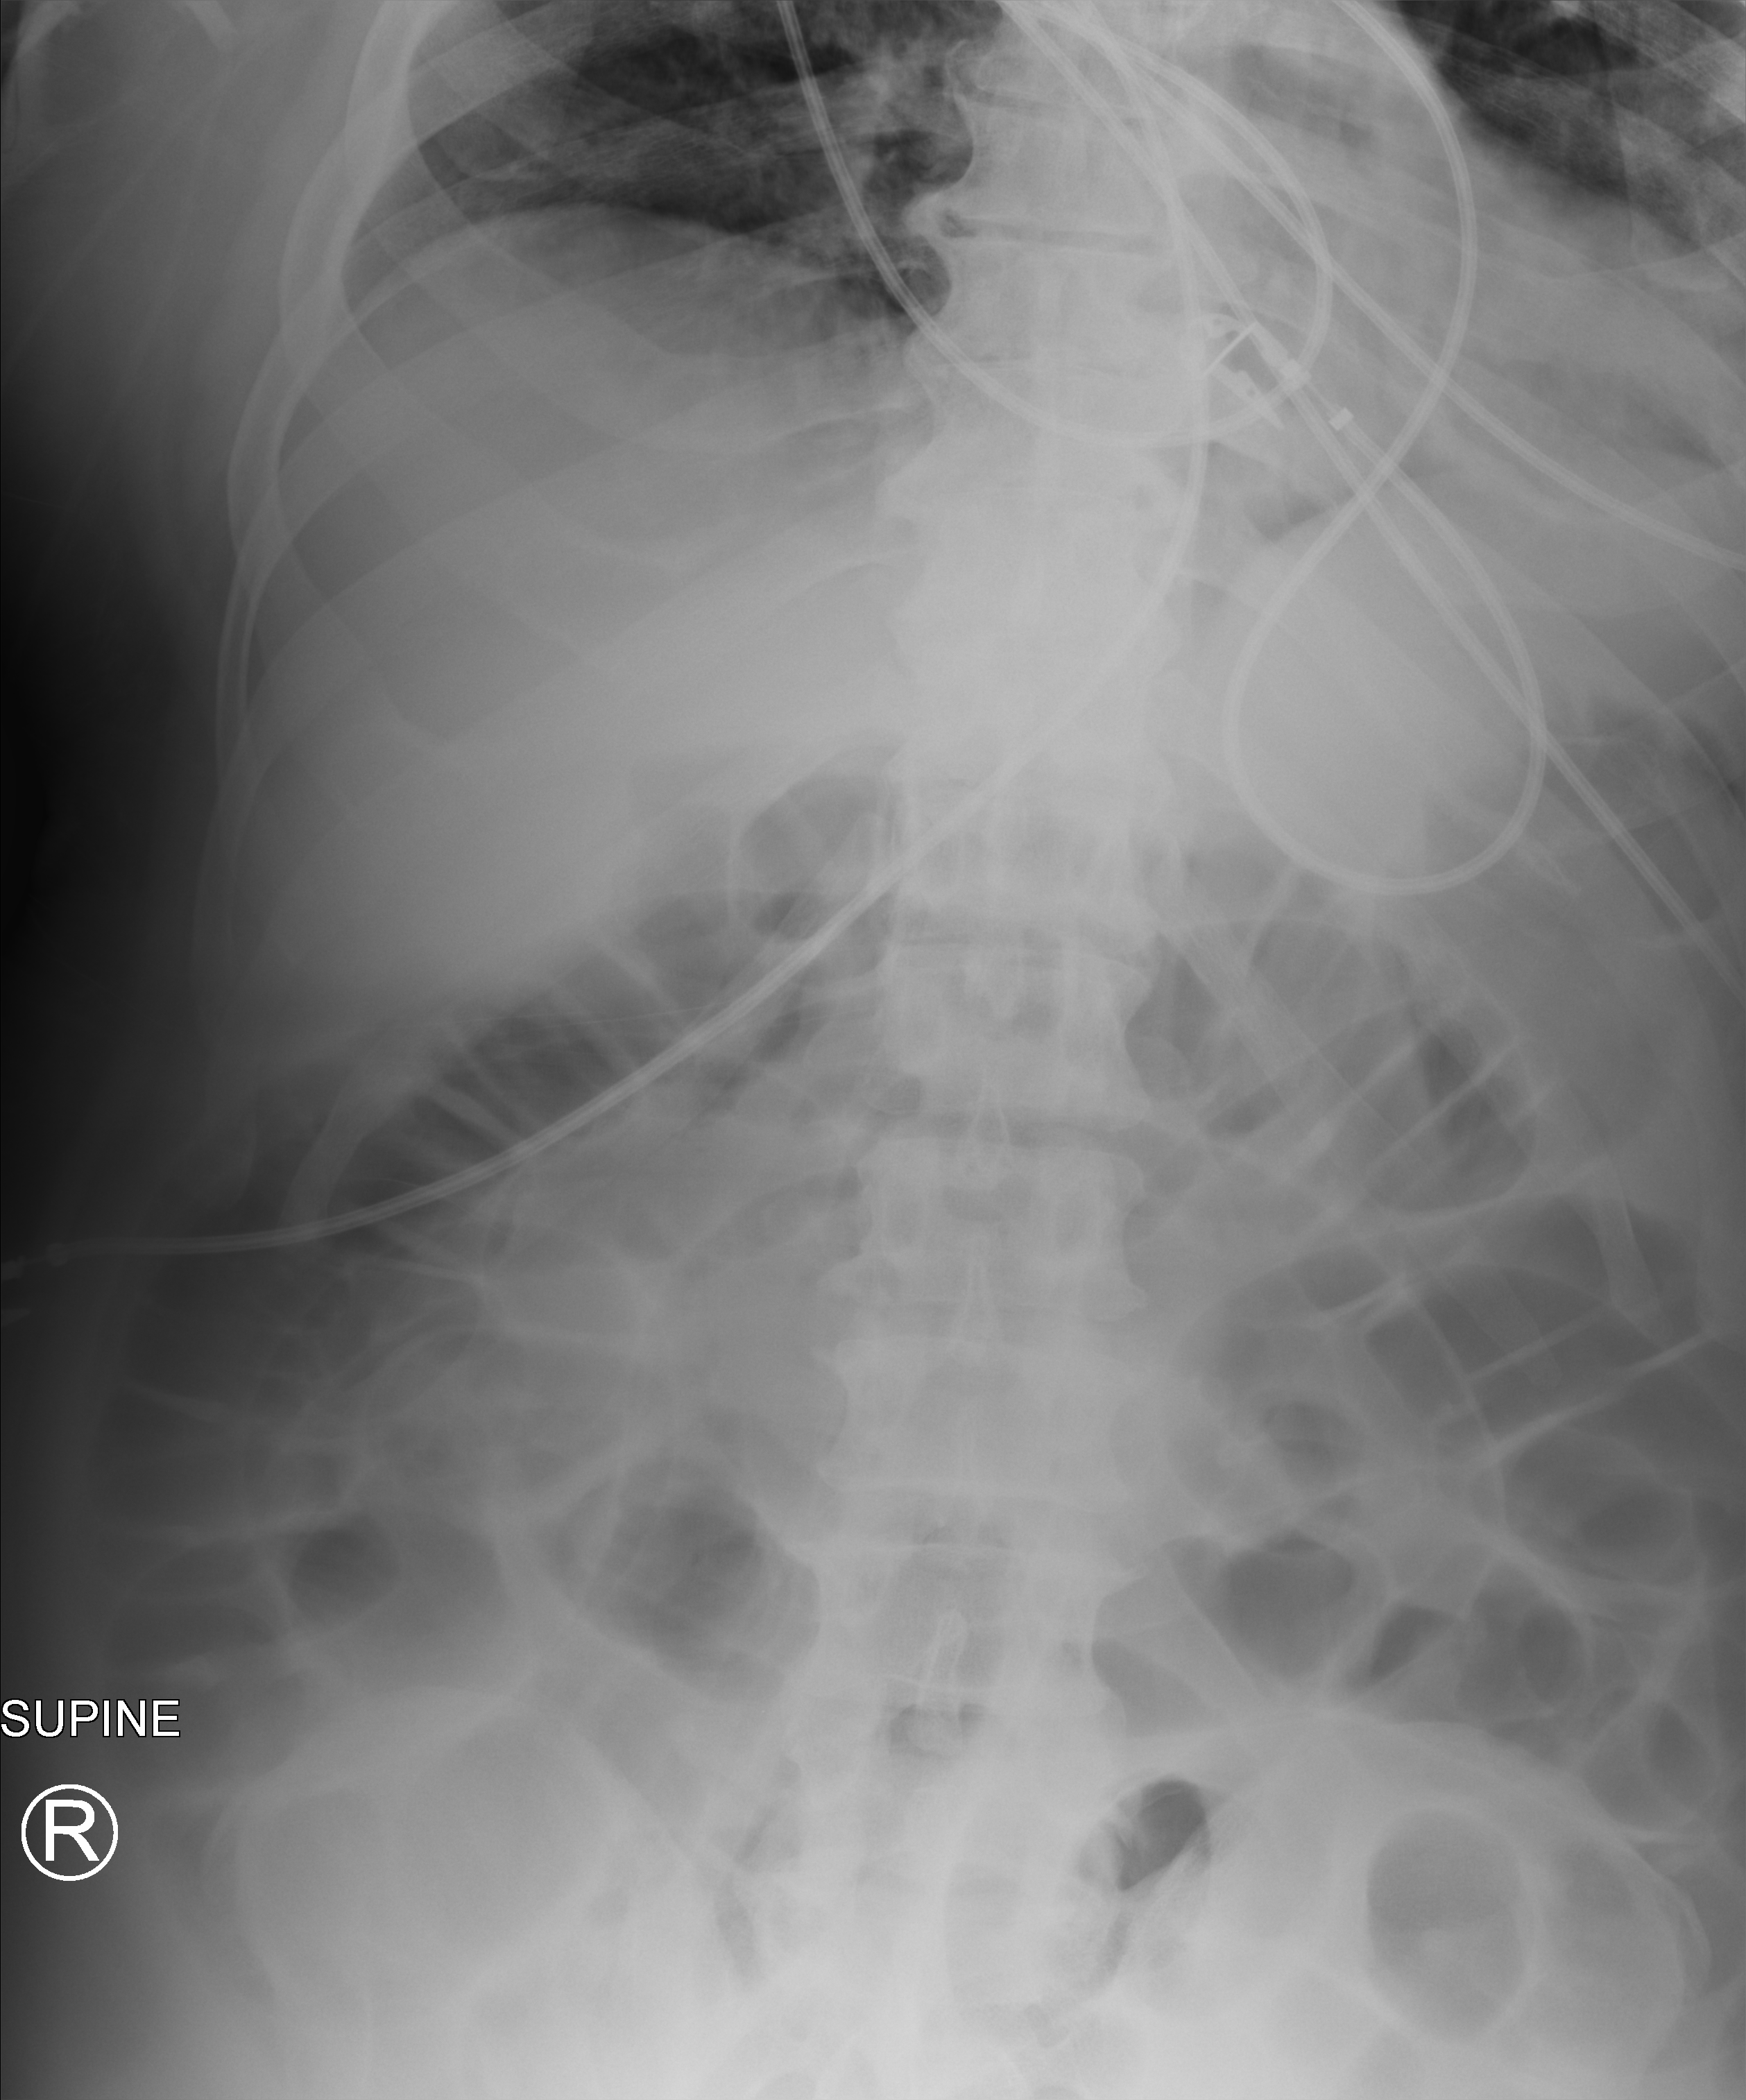
Abdomen X-ray (portable); anteroposterior (AP) projection. Male patient hospitalised with COVID-19, age 18–59 years.
Admission-level facts for this patient (not findings on this image; timing relative to this image not recorded):
- diabetes (admission record): no
- smoking status (admission record): never
- admitted to intensive care during this hospital stay: yes